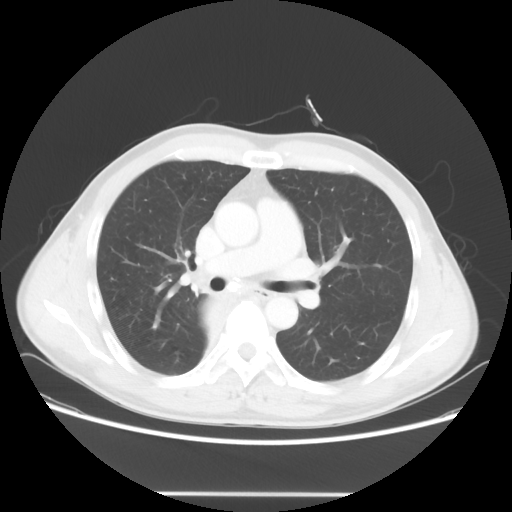
Chest CT, one axial slice; 120 kVp; lung window (W 1500 / L -600 HU); 5 mm slice thickness; 512 × 512 image matrix, field of view 393 × 393 mm. Male patient, age 47 years. From the clinical record (not read from this slice): clinical TNM (as recorded): T2 N0 M0; histopathological grade: G2.
Outlined on this slice (bounding box drawn by a radiologist):
- lung tumour (recorded histology: squamous cell carcinoma): bounding box (x1, y1, x2, y2) in pixels: (190, 280, 239, 351)